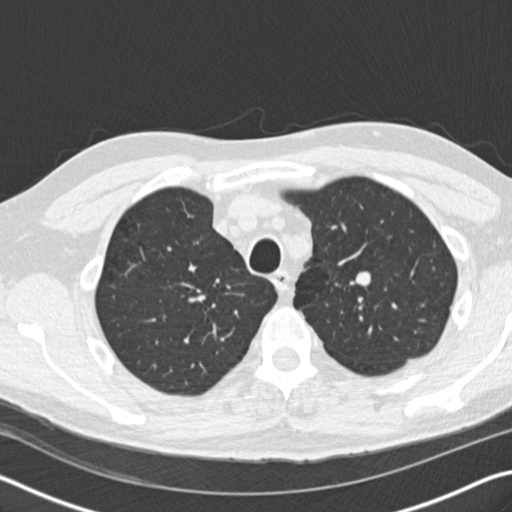
Chest CT (low-dose screening protocol), one axial image. First (baseline) screen. Lung window (W 1500 / L -600 HU). 2 mm slice thickness. Slice 43 of 208 in the series. 512 × 512 image matrix. Male participant, aged 56 years at enrolment.
Expert reader's lesion annotation, bounding box (x1, y1, x2, y2) in pixels: (332, 261, 390, 306). The exam's reader record, not a measurement of the box and not confirmed to be the same lesion: non-calcified nodule or mass ≥4 mm, left upper lobe, 12 × 10 mm, smooth margins, soft tissue attenuation. Official screen result: positive, change unspecified: nodule(s) >= 4 mm or enlarging nodule(s), mass(es), or other non-specific abnormalities suspicious for lung cancer.